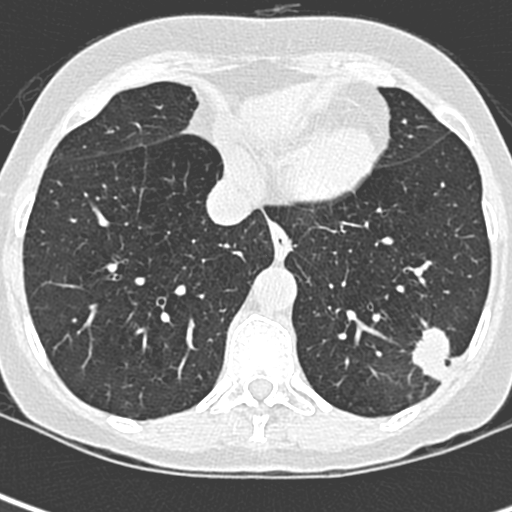
Low-dose screening chest CT, one axial slice; lung window (W 1500 / L -600 HU); 1.3 mm slice thickness; 512 × 512 image matrix, field of view 271 × 271 mm.
Outlined on this slice (manually delineated by an expert):
- lesion 1 (tumor, lower lobe of left lung): bounding box (x1, y1, x2, y2) in pixels: (411, 326, 454, 383)